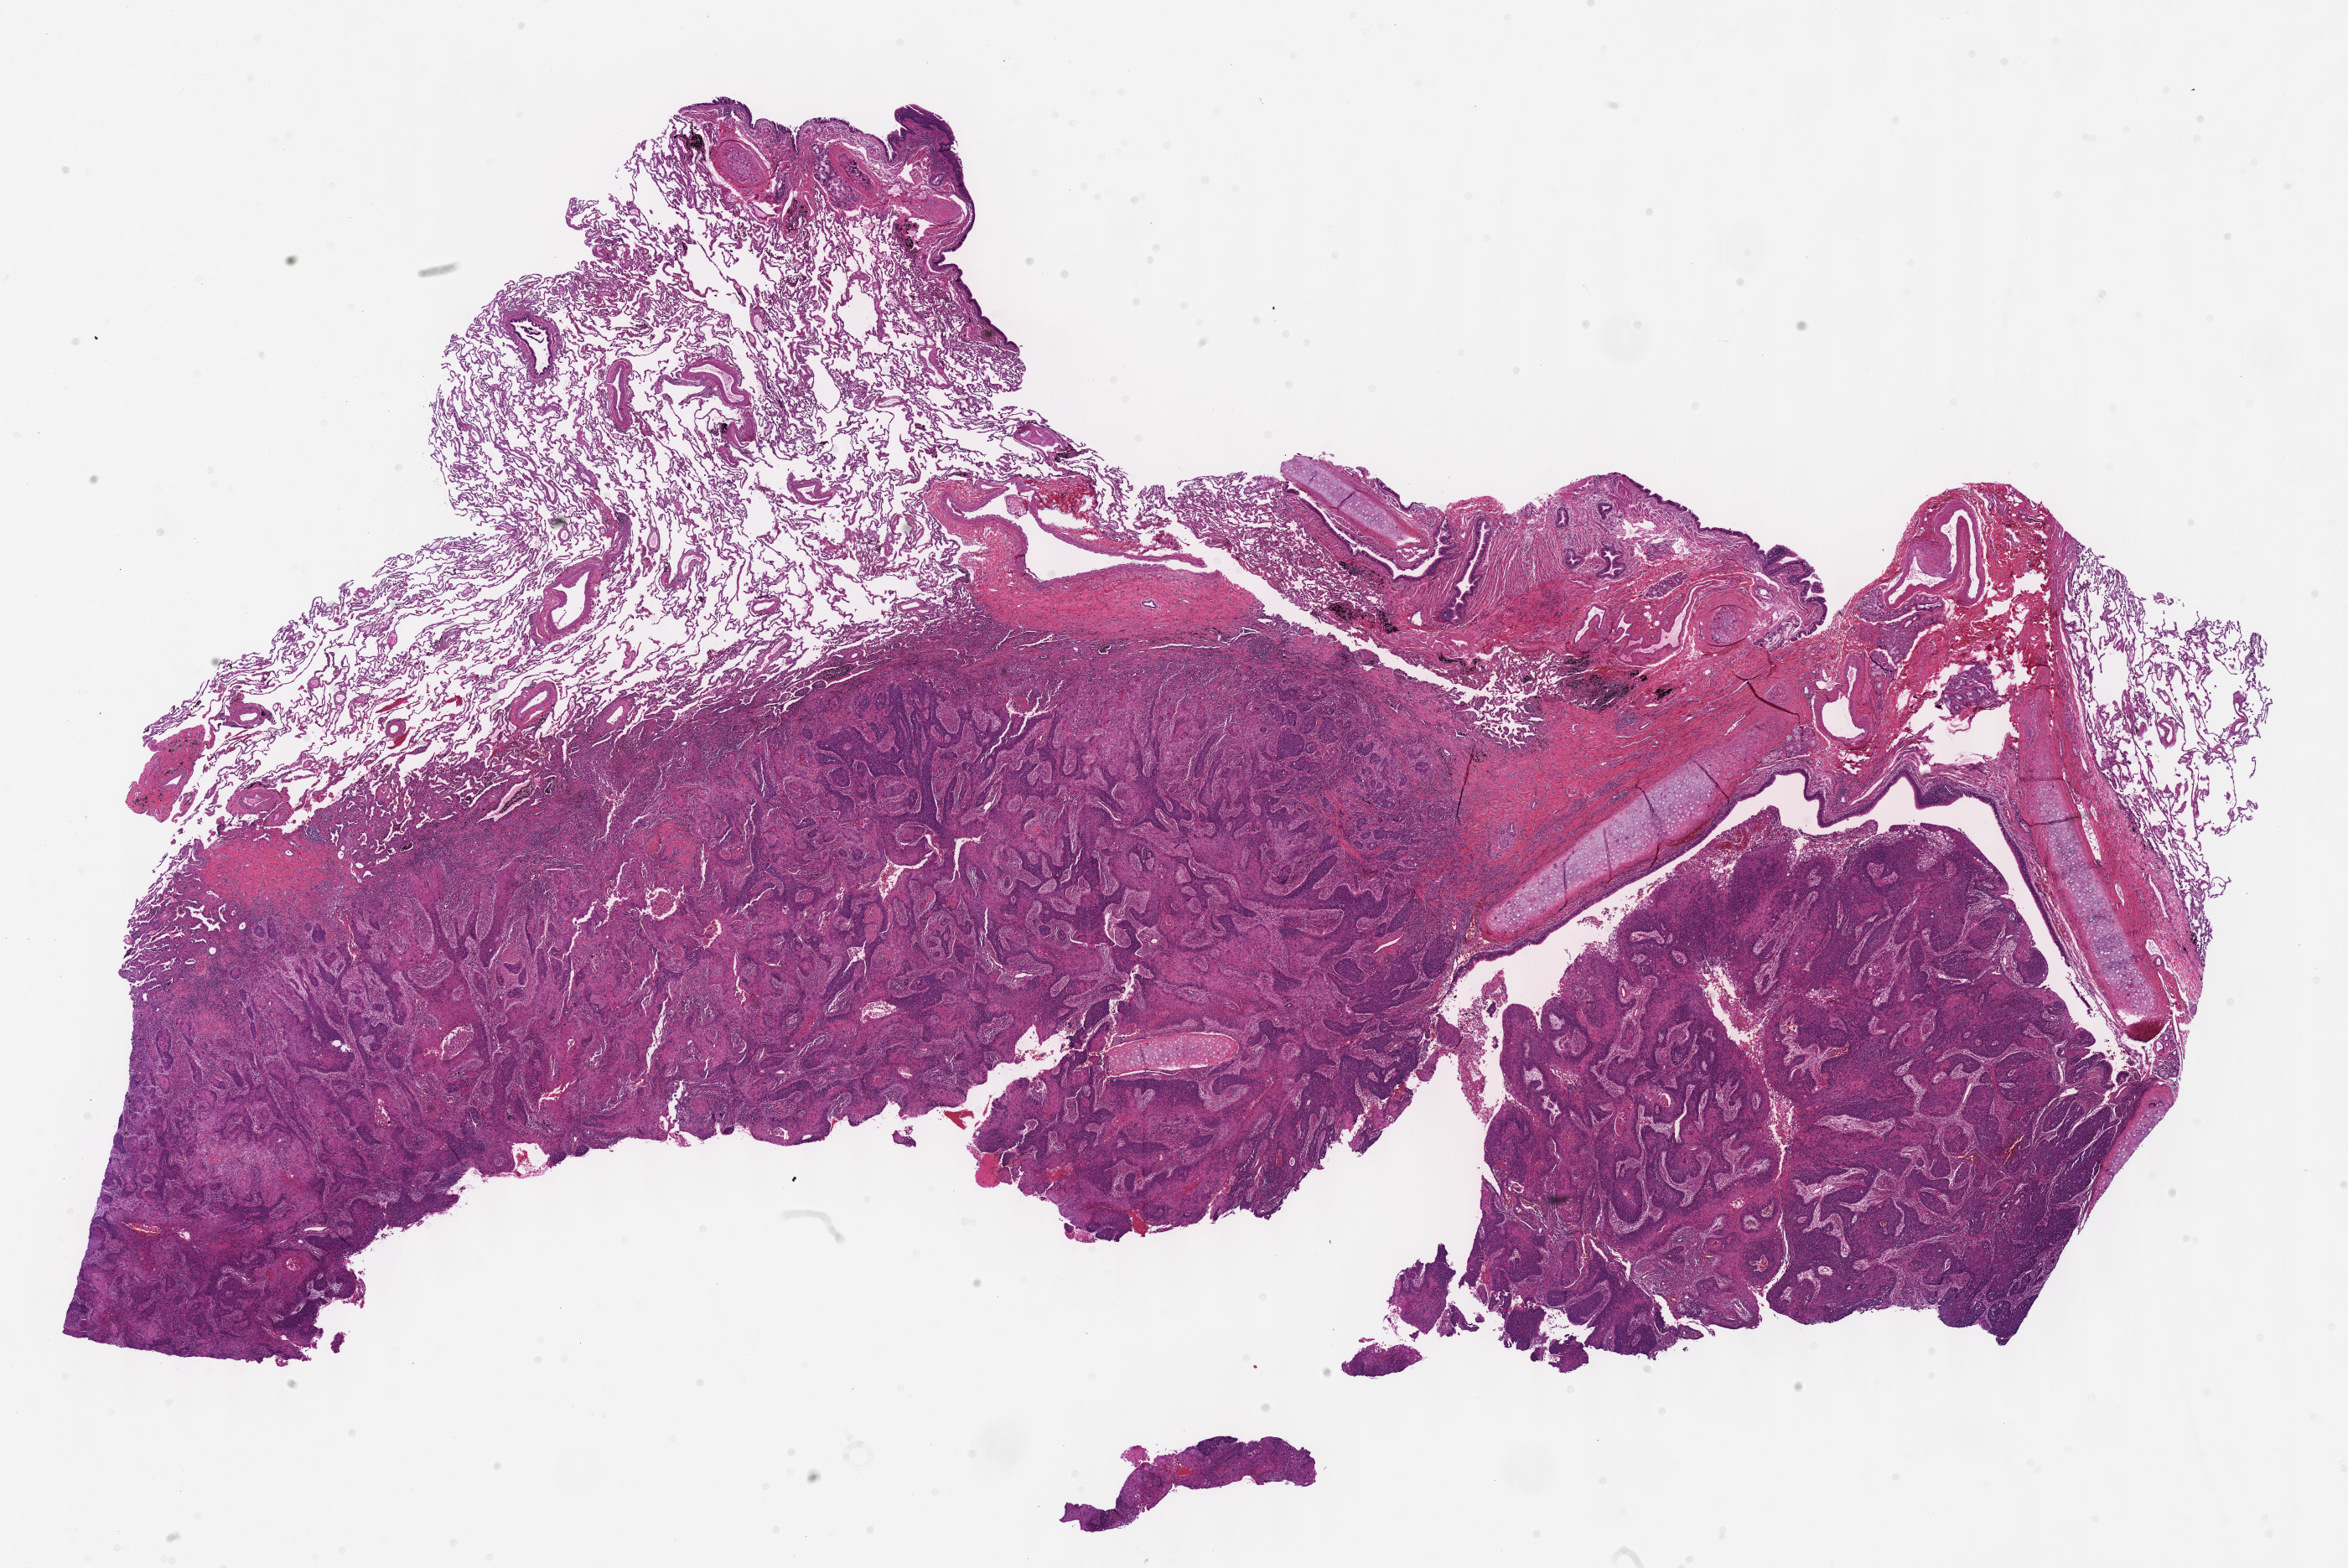
Digitized H&E tissue section (whole slide), whole scanned area (about 22.6 x 15.1 mm) shown as a low-resolution overview, formalin-fixed paraffin-embedded (FFPE) diagnostic section, sample: primary tumour, lung. Male patient.
AJCC pathologic stage: IA (5th edition). Histologic diagnosis: Squamous cell carcinoma, NOS (lower lobe, lung). TNM: T1 N0 MX.